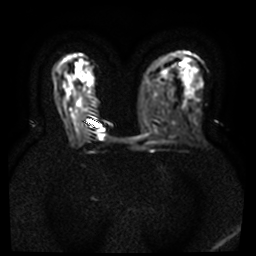
Breast MRI, one axial slice; slice 21 of 40 in the series (ordered by position); diffusion-weighted series; image 2 of 4 stored at this slice position (different b-values; order by instance number); 3 T; 5 mm slice thickness; 256 × 256 image matrix, field of view 340 × 340 mm. Female patient.
Outlined on this slice (manually delineated by an expert):
- tumour on diffusion-weighted imaging: bounding box (x1, y1, x2, y2) in pixels: (100, 135, 103, 138)